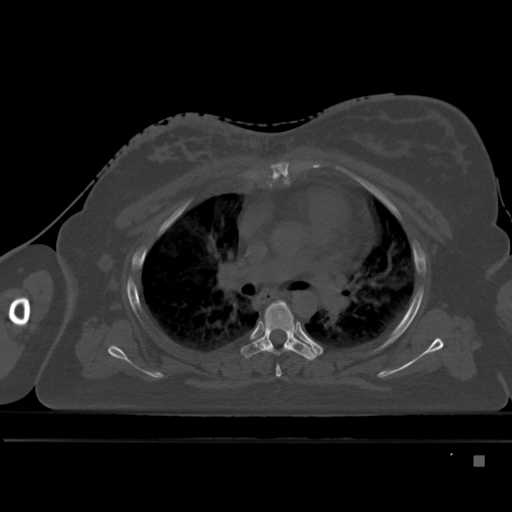
CT including the spine, one axial slice; bone window (W 1800 / L 400 HU); 1.5 mm slice thickness; 512 × 512 image matrix. Patient: female, 33 years. Case-level facts recorded for this patient, not image findings: primary cancer: breast; vertebrae with lytic lesions (as recorded): T1.
Annotated regions visible in this slice (semi-automatic segmentation, software-assisted and operator-edited):
- T4 vertebra: bounding box (x1, y1, x2, y2) in pixels: (276, 323, 296, 377)
- T5 vertebra: (241, 299, 317, 360)